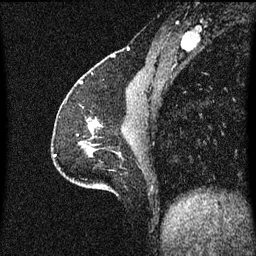
Breast MRI (dynamic contrast-enhanced), one sagittal slice; slice 21 of 60 in the series (ordered by position); dynamic contrast-enhanced series, image 2 of 3 at this slice position (ordered by acquisition); 1.5 T; TE 4.2 ms, TR 8.4 ms; 256 × 256 image matrix, field of view 200 × 200 mm. Female patient, age 51 years.
Outlined on this slice (semi-automatic segmentation, software-assisted and operator-edited):
- analysis volume of interest (the breast-tissue region the enhancement analysis was run in; not a lesion): box from (x=87, y=120) to (x=101, y=139) px
- tumour enhancement mask (voxels above the 70 % enhancement threshold inside the analysis volume of interest): (x=89, y=120)–(x=101, y=133)